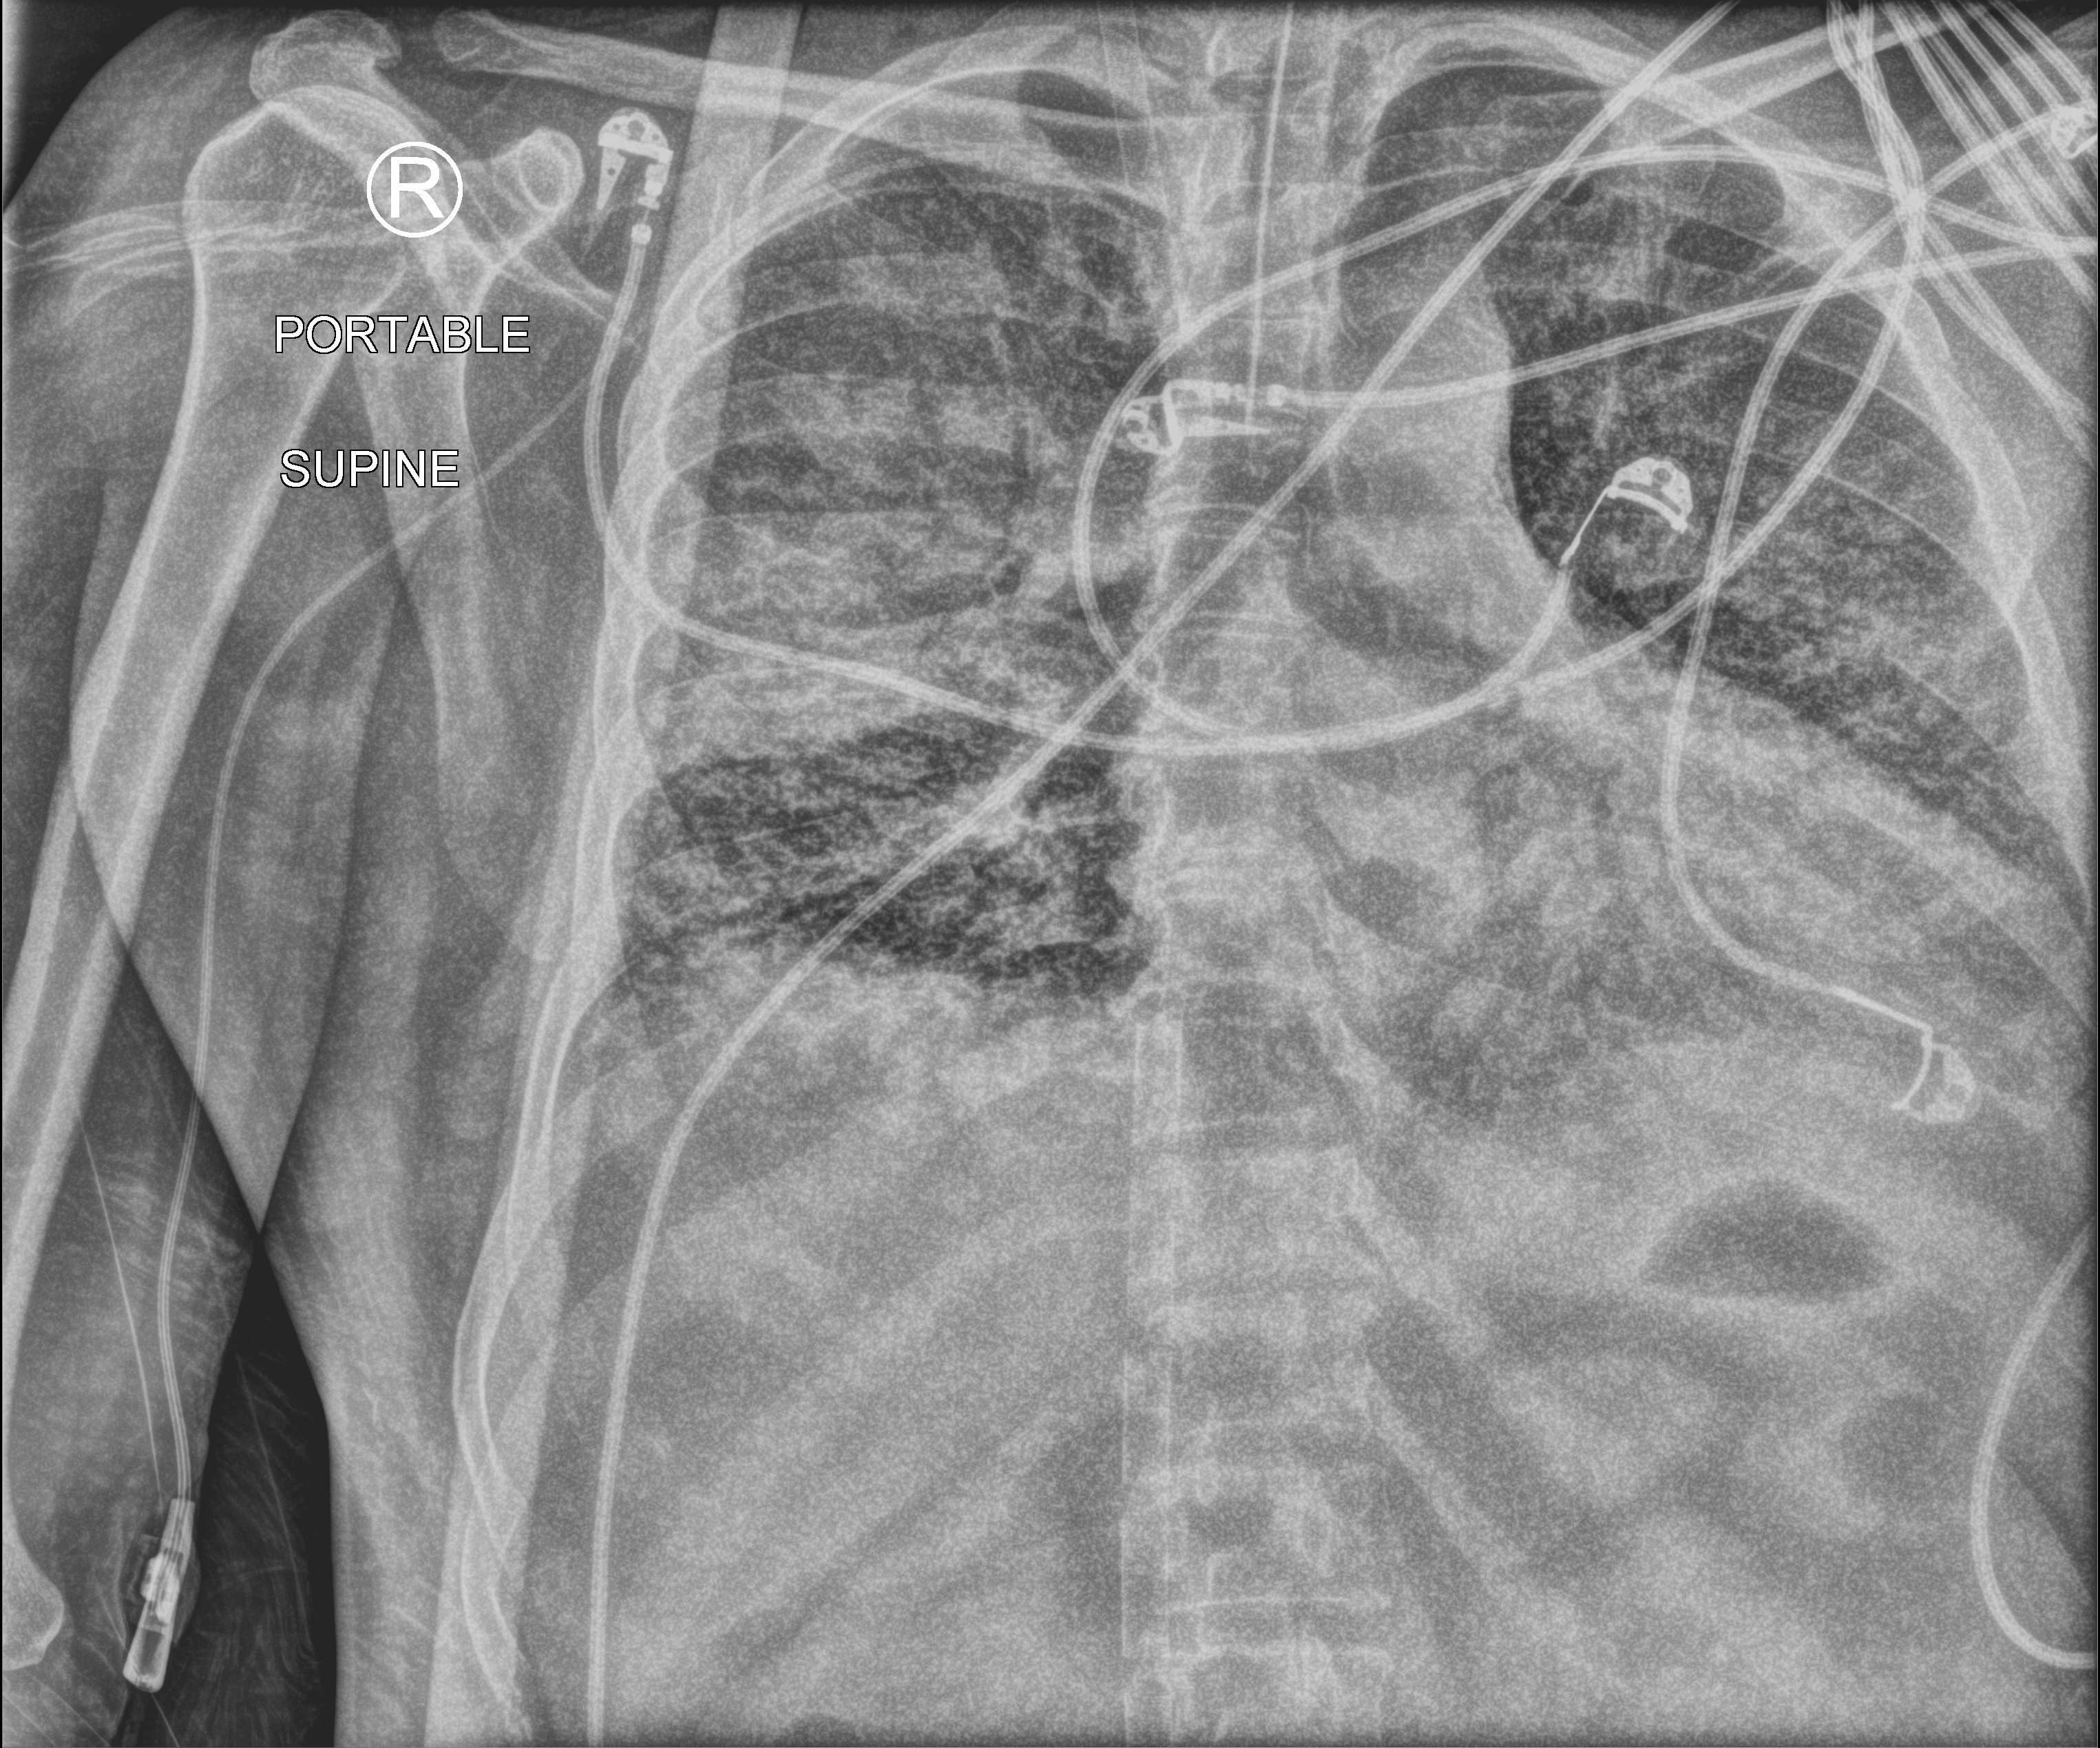
Chest X-ray (portable); anteroposterior (AP) projection. Male patient hospitalised with COVID-19, age 18–59 years.
Hospital-stay facts (about this admission, not read from this image; timing relative to this image not recorded): COPD (admission record): no; mechanically ventilated during this hospital stay: yes.